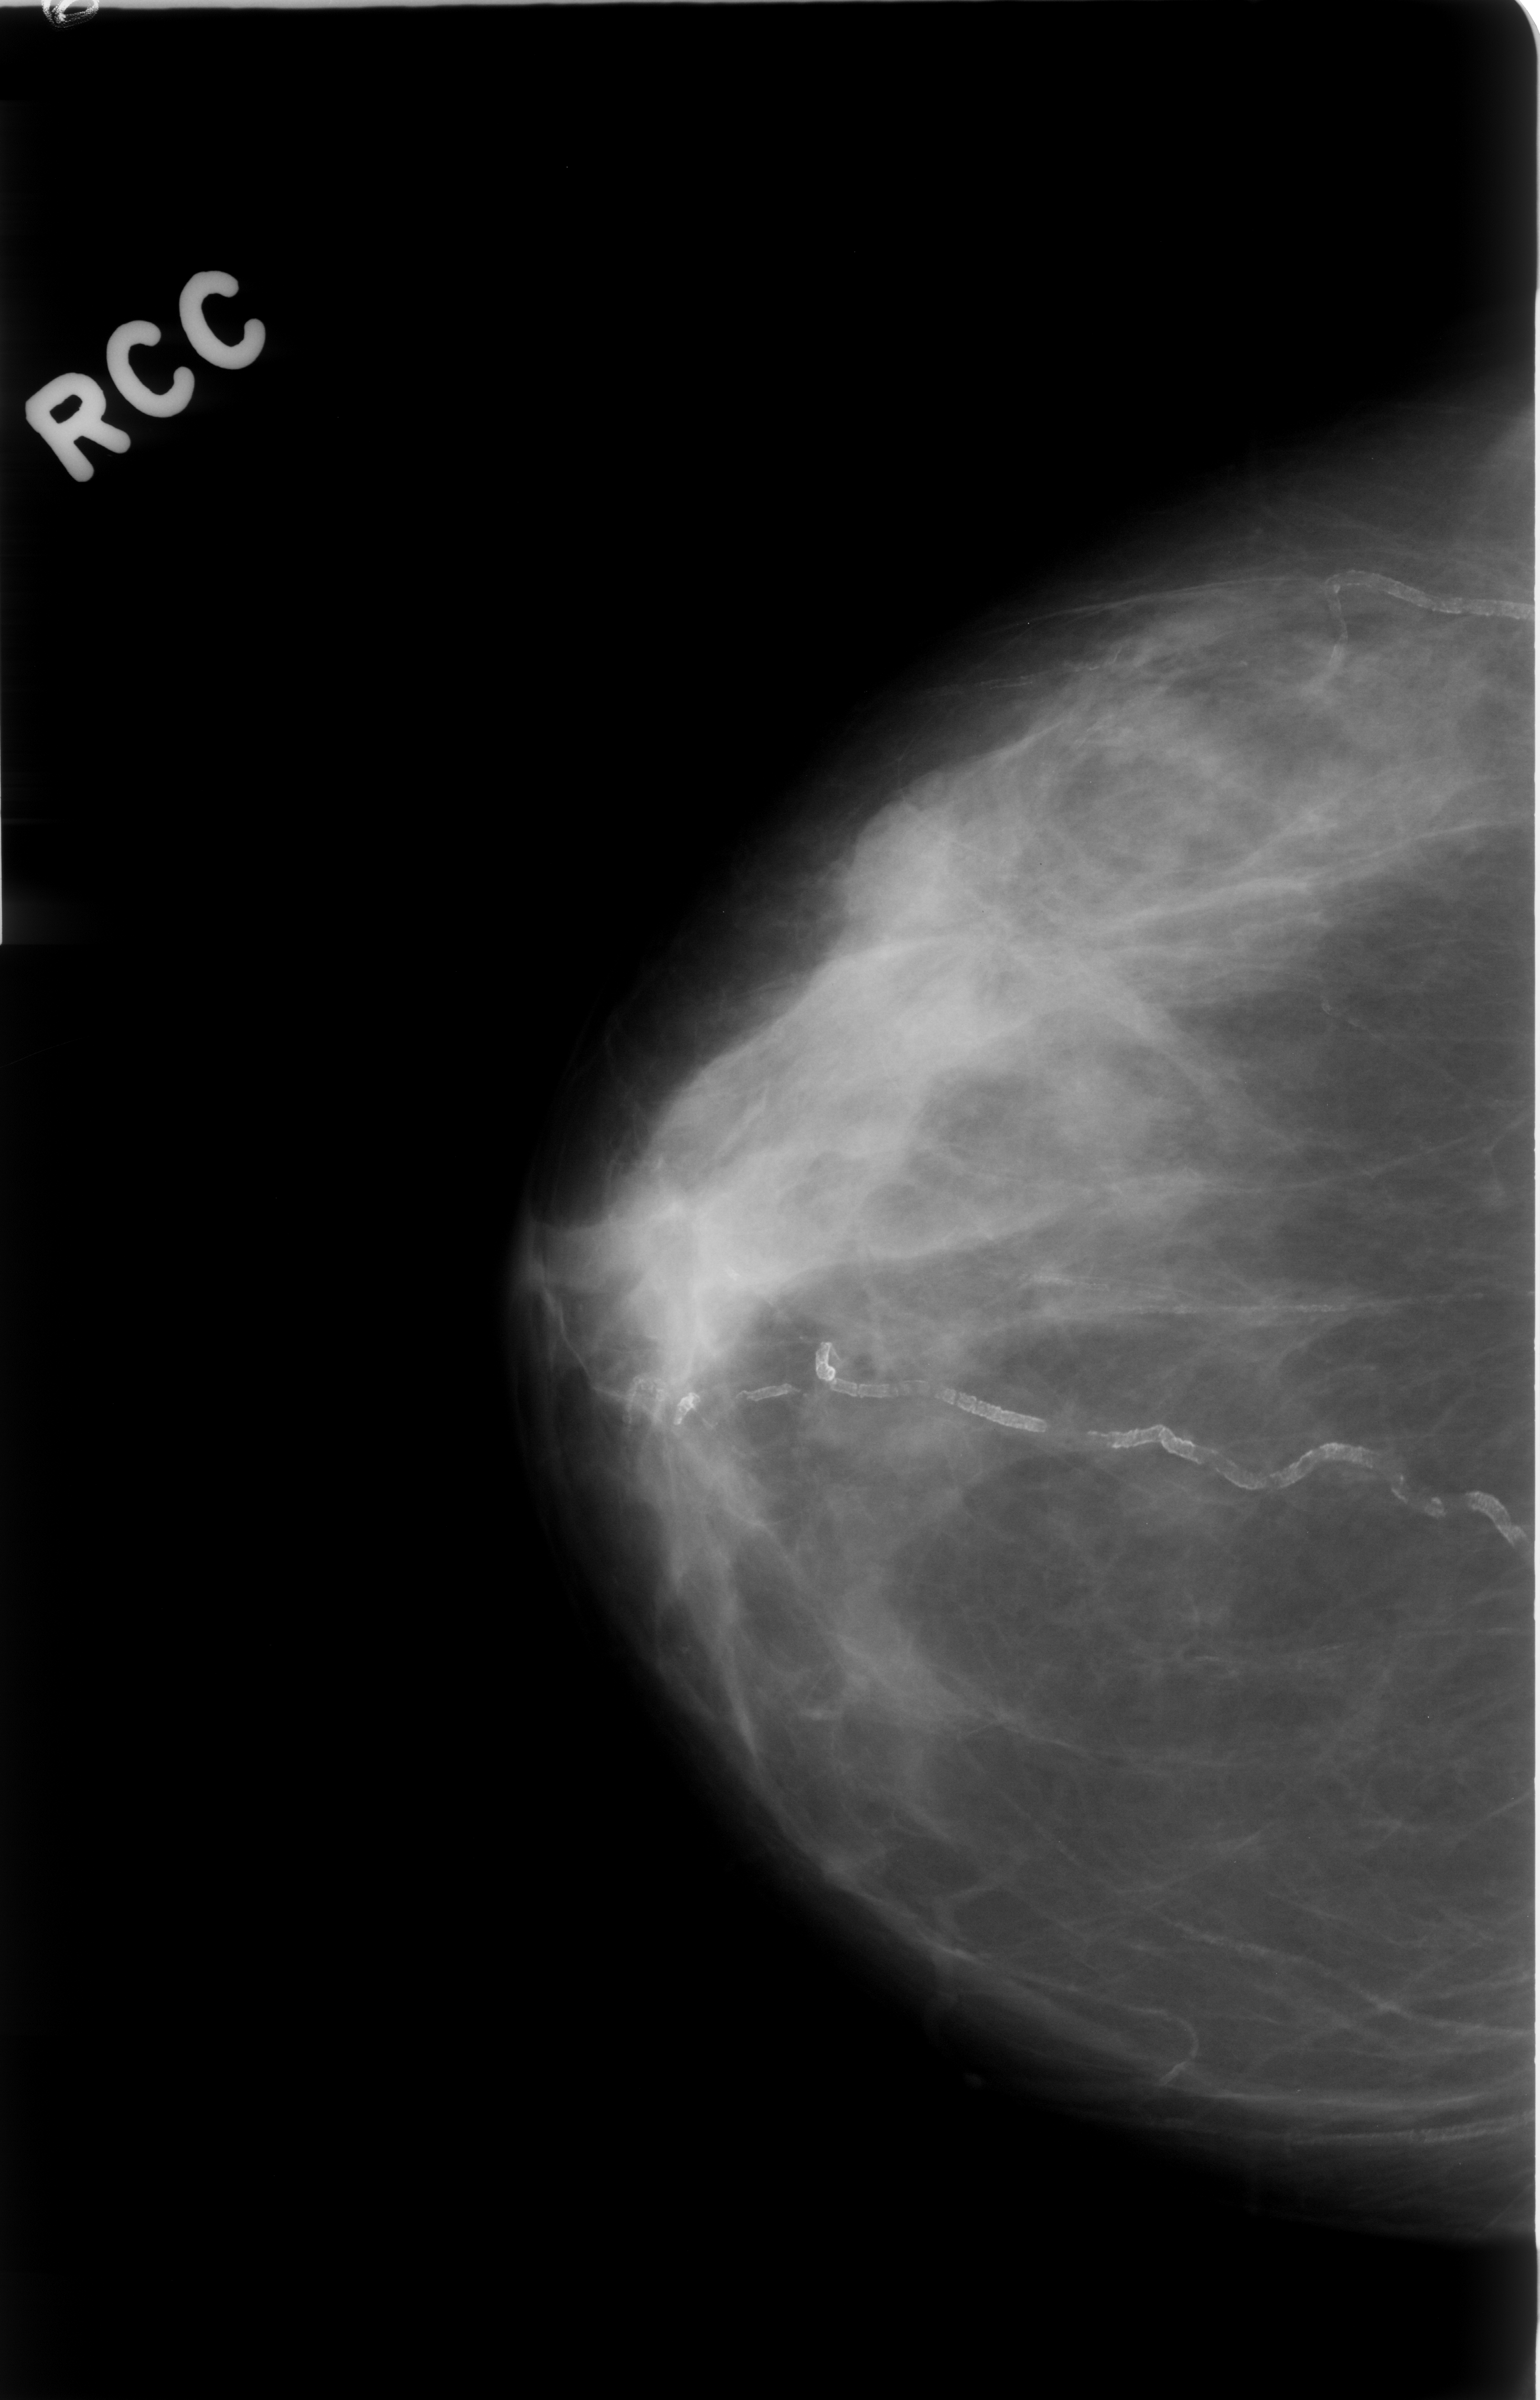
Mammogram (digitized film), right breast, CC view, BI-RADS breast density category 2 (scale 1–4).
Mass, shape architectural distortion; BI-RADS assessment category 4; benign; no additional work-up was recommended (benign without callback).